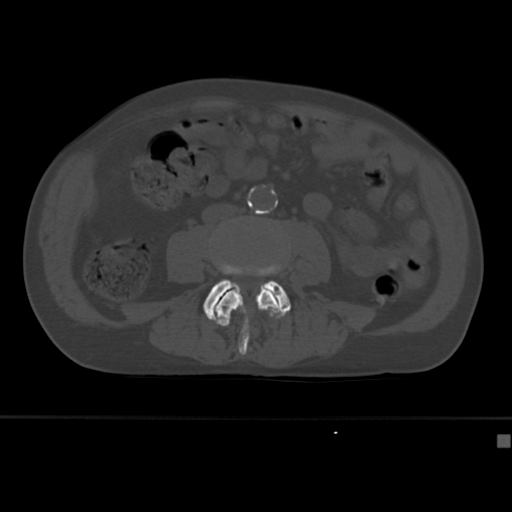
CT including the spine, one axial slice. Position 116 of 430 along the scan axis. Reconstruction kernel Br40s. 120 kVp. Bone window (W 1800 / L 400 HU). 1.5 mm slice thickness. 512 × 512 image matrix, field of view 337 × 337 mm. Patient: male, 64 years. From the clinical record (not read from this slice): primary cancer: uterus; vertebrae with lytic lesions (as recorded): T1, T4, T5, T7, L5.
Structures marked on this image (semi-automatically segmented with operator editing):
- L3 vertebra: box from (x=215, y=290) to (x=281, y=356) px
- L4 vertebra: (x=203, y=263)–(x=291, y=325)